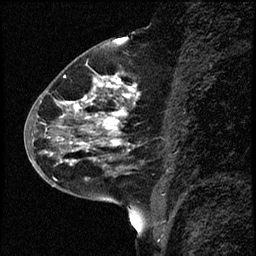
Breast MRI (dynamic contrast-enhanced), one sagittal slice; slice 28 of 68 in the series (ordered by position); dynamic contrast-enhanced study with each time point stored as its own series, time point 2 of 3 at this slice position (early post-contrast, ordered by acquisition time); 1.5 T; TE 4.2 ms, TR 17.6 ms; 256 × 256 image matrix. Female patient, age 52 years. Case-level facts recorded for this patient, not image findings: setting: breast cancer imaged before/during neoadjuvant chemotherapy; receptor status: HER2-positive.
Structures marked on this image (semi-automatically segmented with operator editing):
- analysis volume of interest (the breast-tissue region the enhancement analysis was run in; not a lesion): box from (x=50, y=61) to (x=150, y=184) px
- tumour enhancement mask (voxels above the 100 % enhancement threshold inside the analysis volume of interest): (x=60, y=74)–(x=133, y=164)